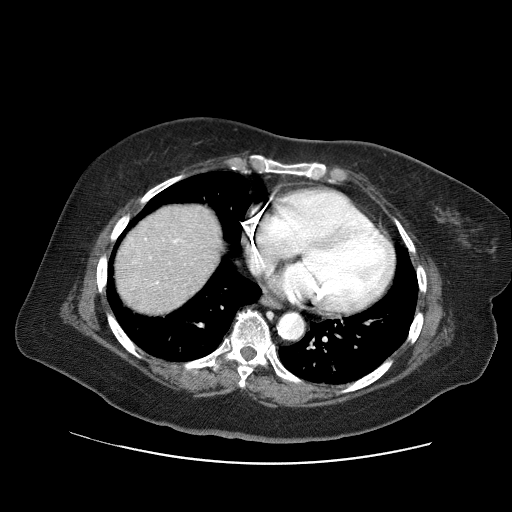
Contrast-enhanced abdominal CT (liver protocol), one axial slice; slice 62 of 71 in the series (ordered by position); soft-tissue window (W 400 / L 40 HU); 2.5 mm slice thickness; 512 × 512 image matrix, field of view 400 × 400 mm. Case-level facts recorded for this patient, not image findings: diagnosis: hepatocellular carcinoma (patient treated with transarterial chemoembolisation; whether this scan precedes or follows treatment is not stated here); TNM stage (as recorded): Stage-II; Child-Pugh class: A.
Structures marked on this image (semi-automatic segmentation, software-assisted and operator-edited):
- abdominal aorta: bounding box <278,313,303,338> (left, top, right, bottom; pixels)
- liver parenchyma outside the tumour (the mass and vessels are separate outlines, so this box may not span the whole liver): <115,204,222,312>
- liver vessels: <145,239,180,284>